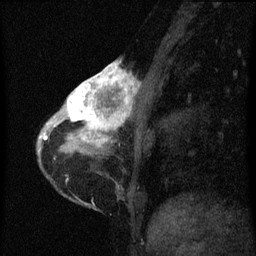
Breast MRI (dynamic contrast-enhanced), one sagittal slice. Slice 17 of 60 in the series (ordered by position). Dynamic contrast-enhanced series, image 2 of 3 at this slice position (ordered by acquisition). 1.5 T. TE 4.2 ms, TR 8 ms. 2 mm slice thickness. 256 × 256 image matrix, field of view 180 × 180 mm. Patient: female, 38 years.
Outlined on this slice (semi-automatic segmentation, software-assisted and operator-edited):
- analysis volume of interest (the breast-tissue region the enhancement analysis was run in; not a lesion): bounding box [x1, y1, x2, y2] px = [61, 64, 144, 147]
- tumour enhancement mask (voxels above the 70 % enhancement threshold inside the analysis volume of interest): [61, 64, 137, 147]